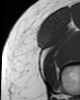
MRI of an extremity soft-tissue mass, one axial slice; slice 10 of 46 in the series (ordered by position); MR volume resampled by the dataset authors to the PET/CT grid (not the native acquisition matrix); 3.27 mm slice thickness; 80 × 100 image matrix, field of view 78 × 98 mm. Female patient. From the clinical record (not read from this slice): histological type: synovial sarcoma; grade: intermediate; site of the primary tumour: right thigh.
Structures marked on this image (expert contour drawn on MRI and transferred to this co-registered scan by the dataset authors):
- gross tumour volume including surrounding oedema: bounding box <37,33,49,47> (left, top, right, bottom; pixels)
- gross tumour volume (mass): <37,33,49,47>